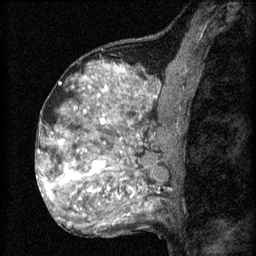
Breast MRI (dynamic contrast-enhanced), one sagittal slice; position 37 of 60 along the scan axis; 3 images stored at this slice position (order not interpretable as contrast timing); 1.5 T; TE 4.2 ms, TR 8.2 ms; 2 mm slice thickness; 256 × 256 image matrix, field of view 180 × 180 mm. Female patient, age 48 years.
Outlined on this slice (semi-automatically segmented with operator editing):
- analysis volume of interest (the breast-tissue region the enhancement analysis was run in; not a lesion): bounding box [x1, y1, x2, y2] px = [61, 138, 153, 201]
- tumour enhancement mask (voxels above the 70 % enhancement threshold inside the analysis volume of interest): [61, 140, 135, 201]